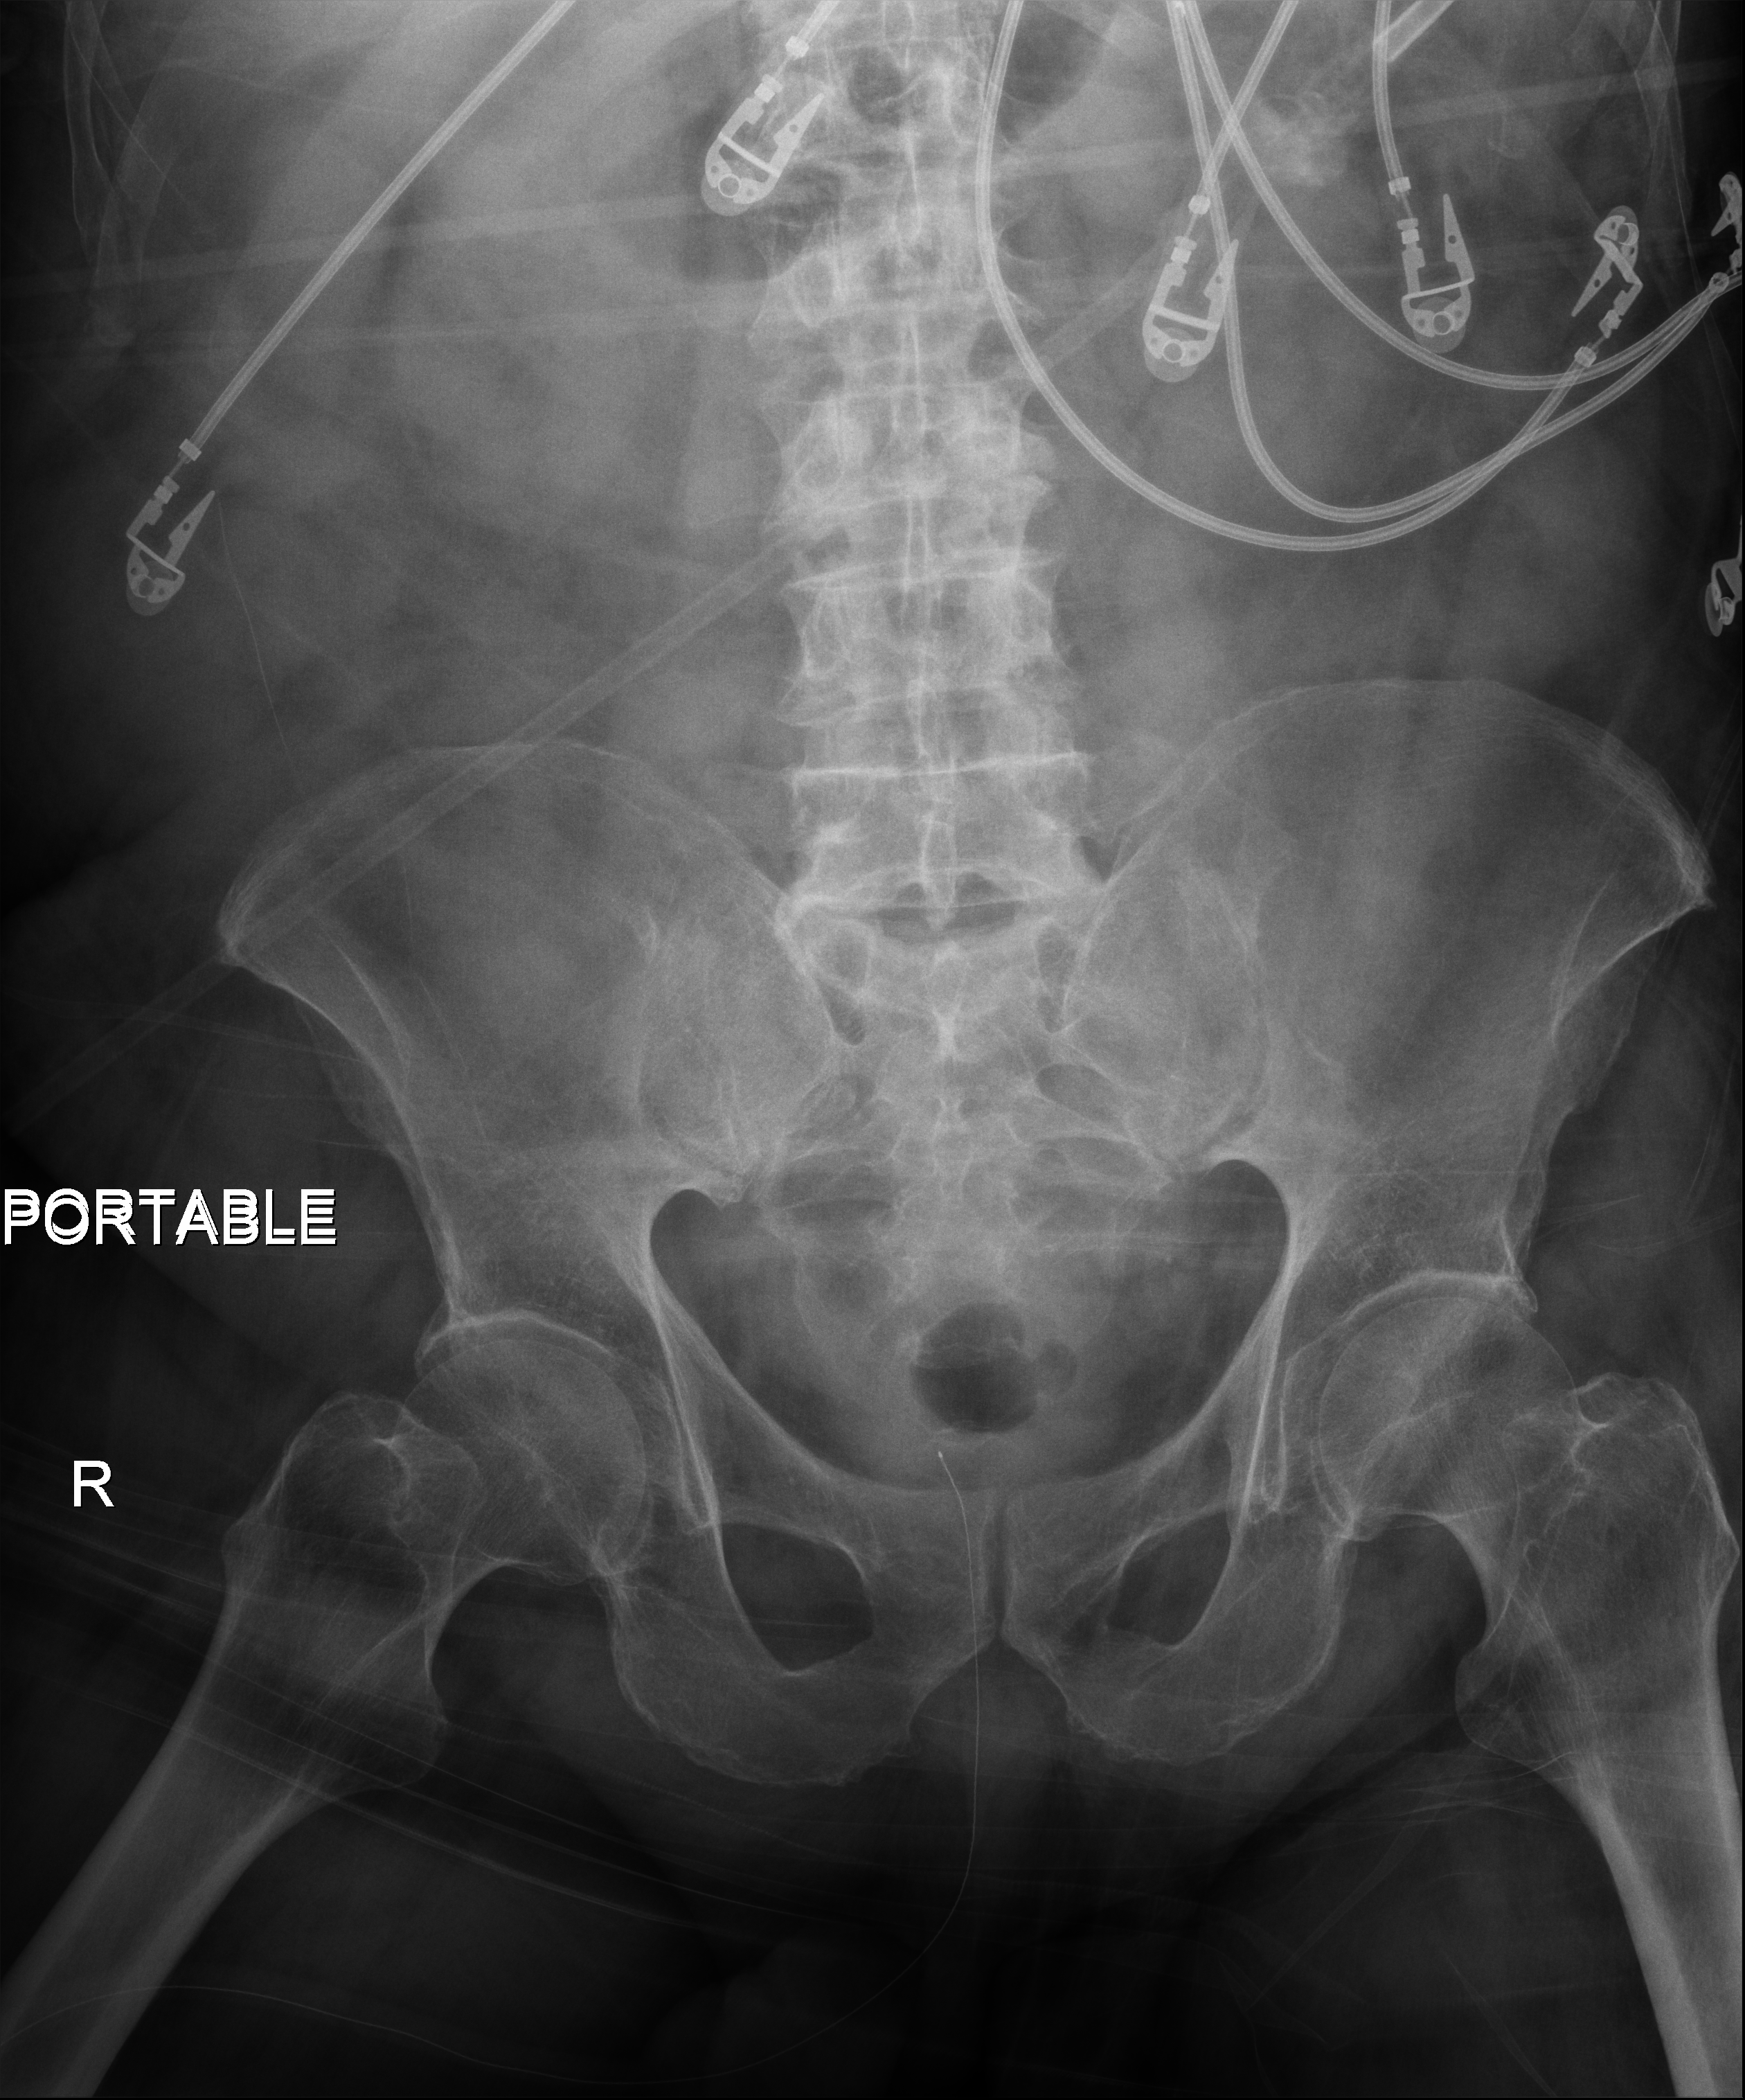
Portable abdomen radiograph. Patient hospitalised with COVID-19; male, aged 75–90 years.
From the hospital-stay record, not from the radiograph (when in the stay this image was taken is not recorded):
- length of hospital stay: 30 days
- mechanically ventilated during this hospital stay: yes